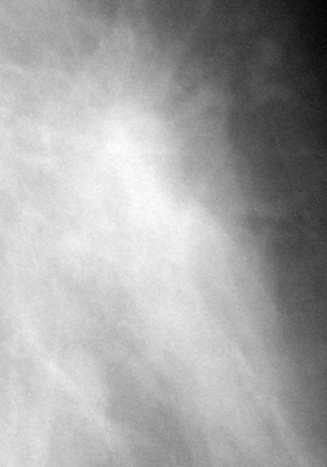
Crop from a digitized film mammogram around one marked abnormality, left breast, MLO view, BI-RADS breast density category 1 (scale 1–4).
Mass, shape irregular, margins spiculated; BI-RADS assessment category 4; subtlety rating 5 on a 1 (subtle) to 5 (obvious) scale; benign; no additional work-up was recommended (benign without callback).